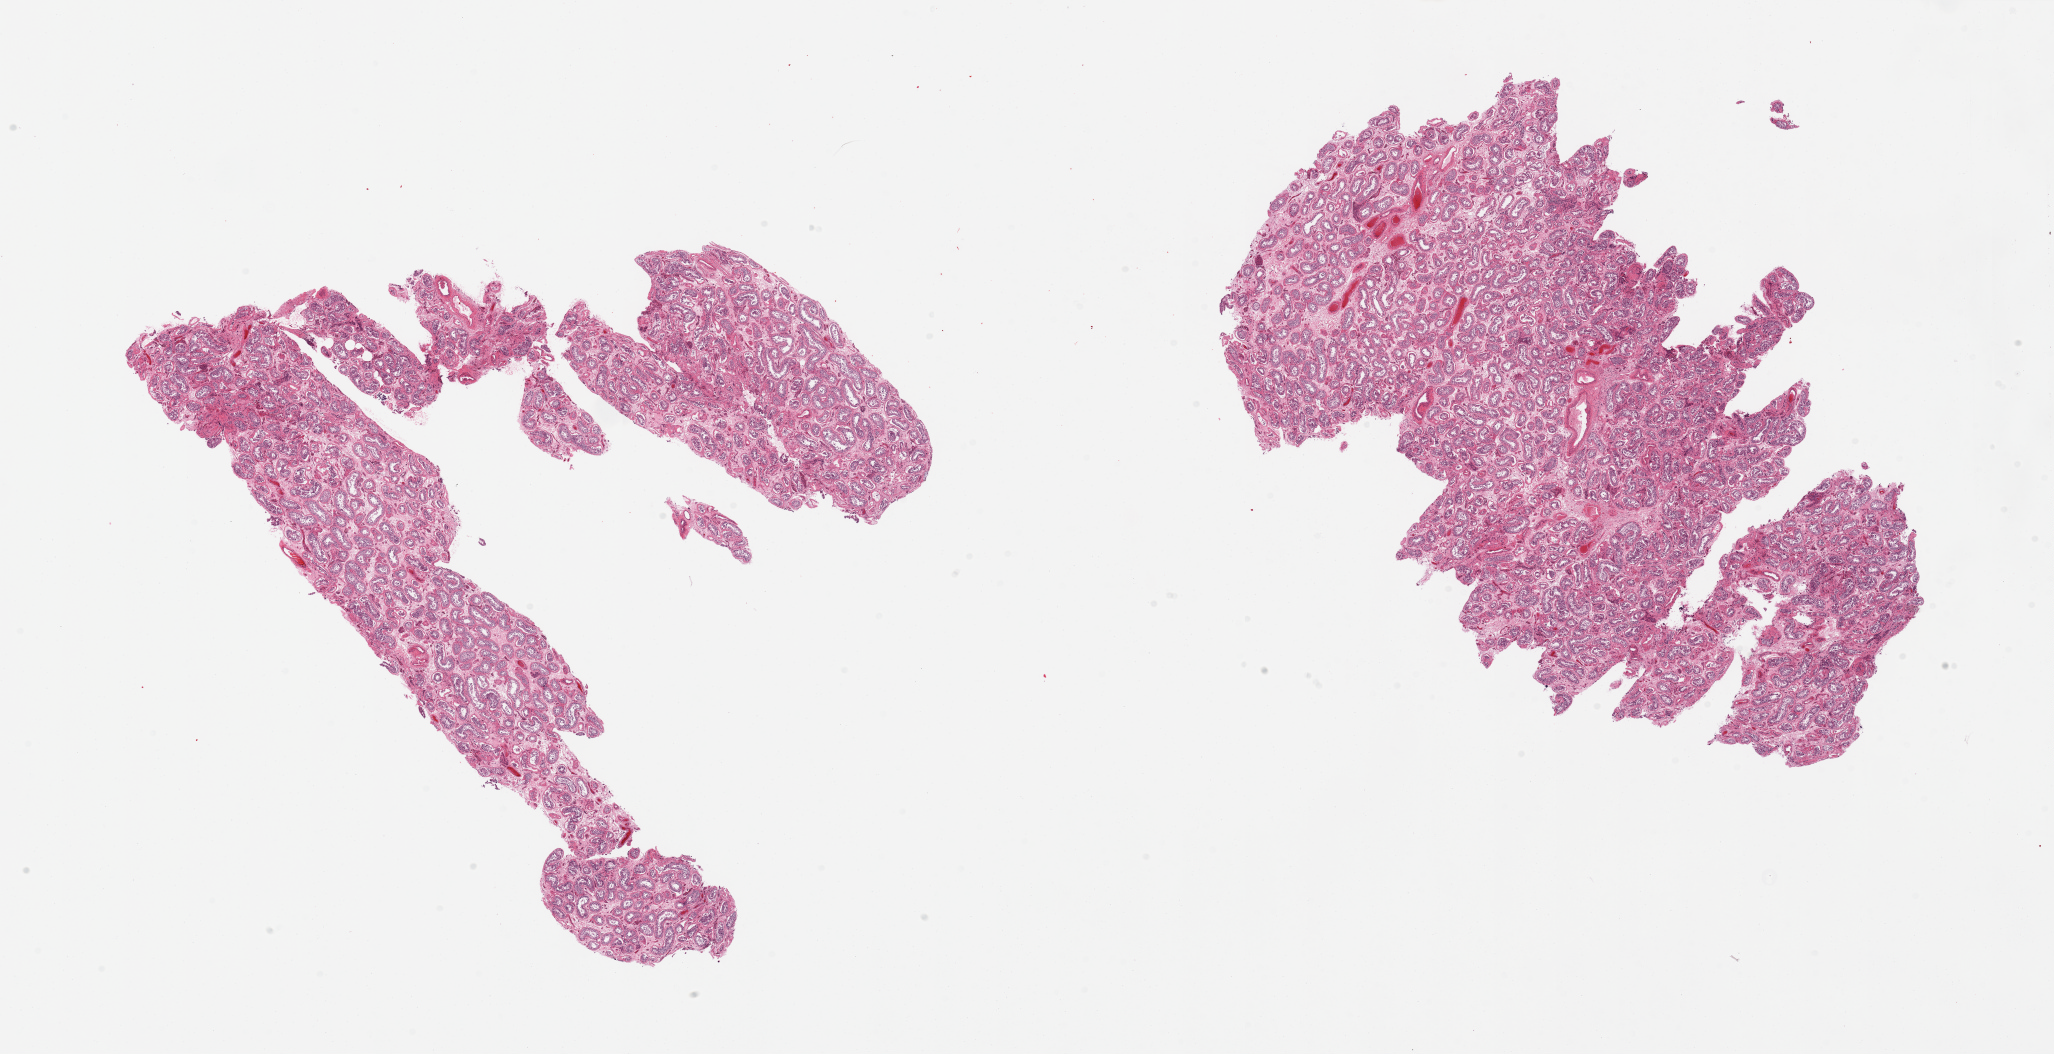
Digitized H&E-stained section — shown as a low-resolution overview of the whole scanned area (about 32.5 x 16.7 mm); PAXgene-fixed, paraffin-embedded tissue; target tissue: testis; tissue donor sample. Male donor.
Review note (as recorded): 2 pieces; reduced spermatogenesis.